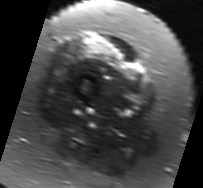
MRI of an extremity soft-tissue mass, one axial slice. Slice 18 of 91 in the series (ordered by position). T2-weighted fat-saturated. MR volume resampled by the dataset authors to the PET/CT grid (not the native acquisition matrix). 3.27 mm slice thickness. 203 × 188 image matrix. Female patient. From the clinical record (not read from this slice): histological type: malignant solitary fibrous tumor; grade: intermediate; site of the primary tumour: right thigh.
Outlined on this slice (expert contour drawn on MRI and transferred to this co-registered scan by the dataset authors):
- gross tumour volume including surrounding oedema: bounding box <79,35,137,77> (left, top, right, bottom; pixels)